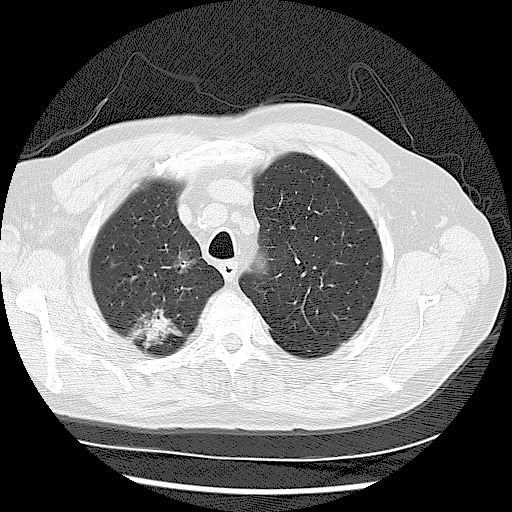
Low-dose screening chest CT, one axial slice; position 95 of 122 along the scan axis; lung window (W 1500 / L -600 HU); 512 × 512 image matrix.
Outlined on this slice (expert manual segmentation):
- lesion 1 (tumor, upper lobe of right lung): bounding box [x1, y1, x2, y2] px = [129, 310, 181, 348]